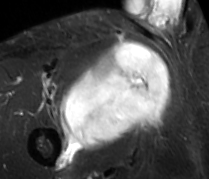
MRI of an extremity soft-tissue mass, one axial slice; slice 57 of 89 in the series (ordered by position); STIR; MR volume resampled by the dataset authors to the PET/CT grid (not the native acquisition matrix); 3.27 mm slice thickness; 209 × 179 image matrix, field of view 204 × 175 mm. Male patient. From the clinical record (not read from this slice): histological type: undifferentiated - pleiomorphic; grade: high; site of the primary tumour: right thigh.
Structures marked on this image (expert contour drawn on MRI and transferred to this co-registered scan by the dataset authors):
- gross tumour volume including surrounding oedema: bounding box (x1, y1, x2, y2) in pixels: (60, 41, 170, 149)
- gross tumour volume (mass): (60, 41, 170, 149)